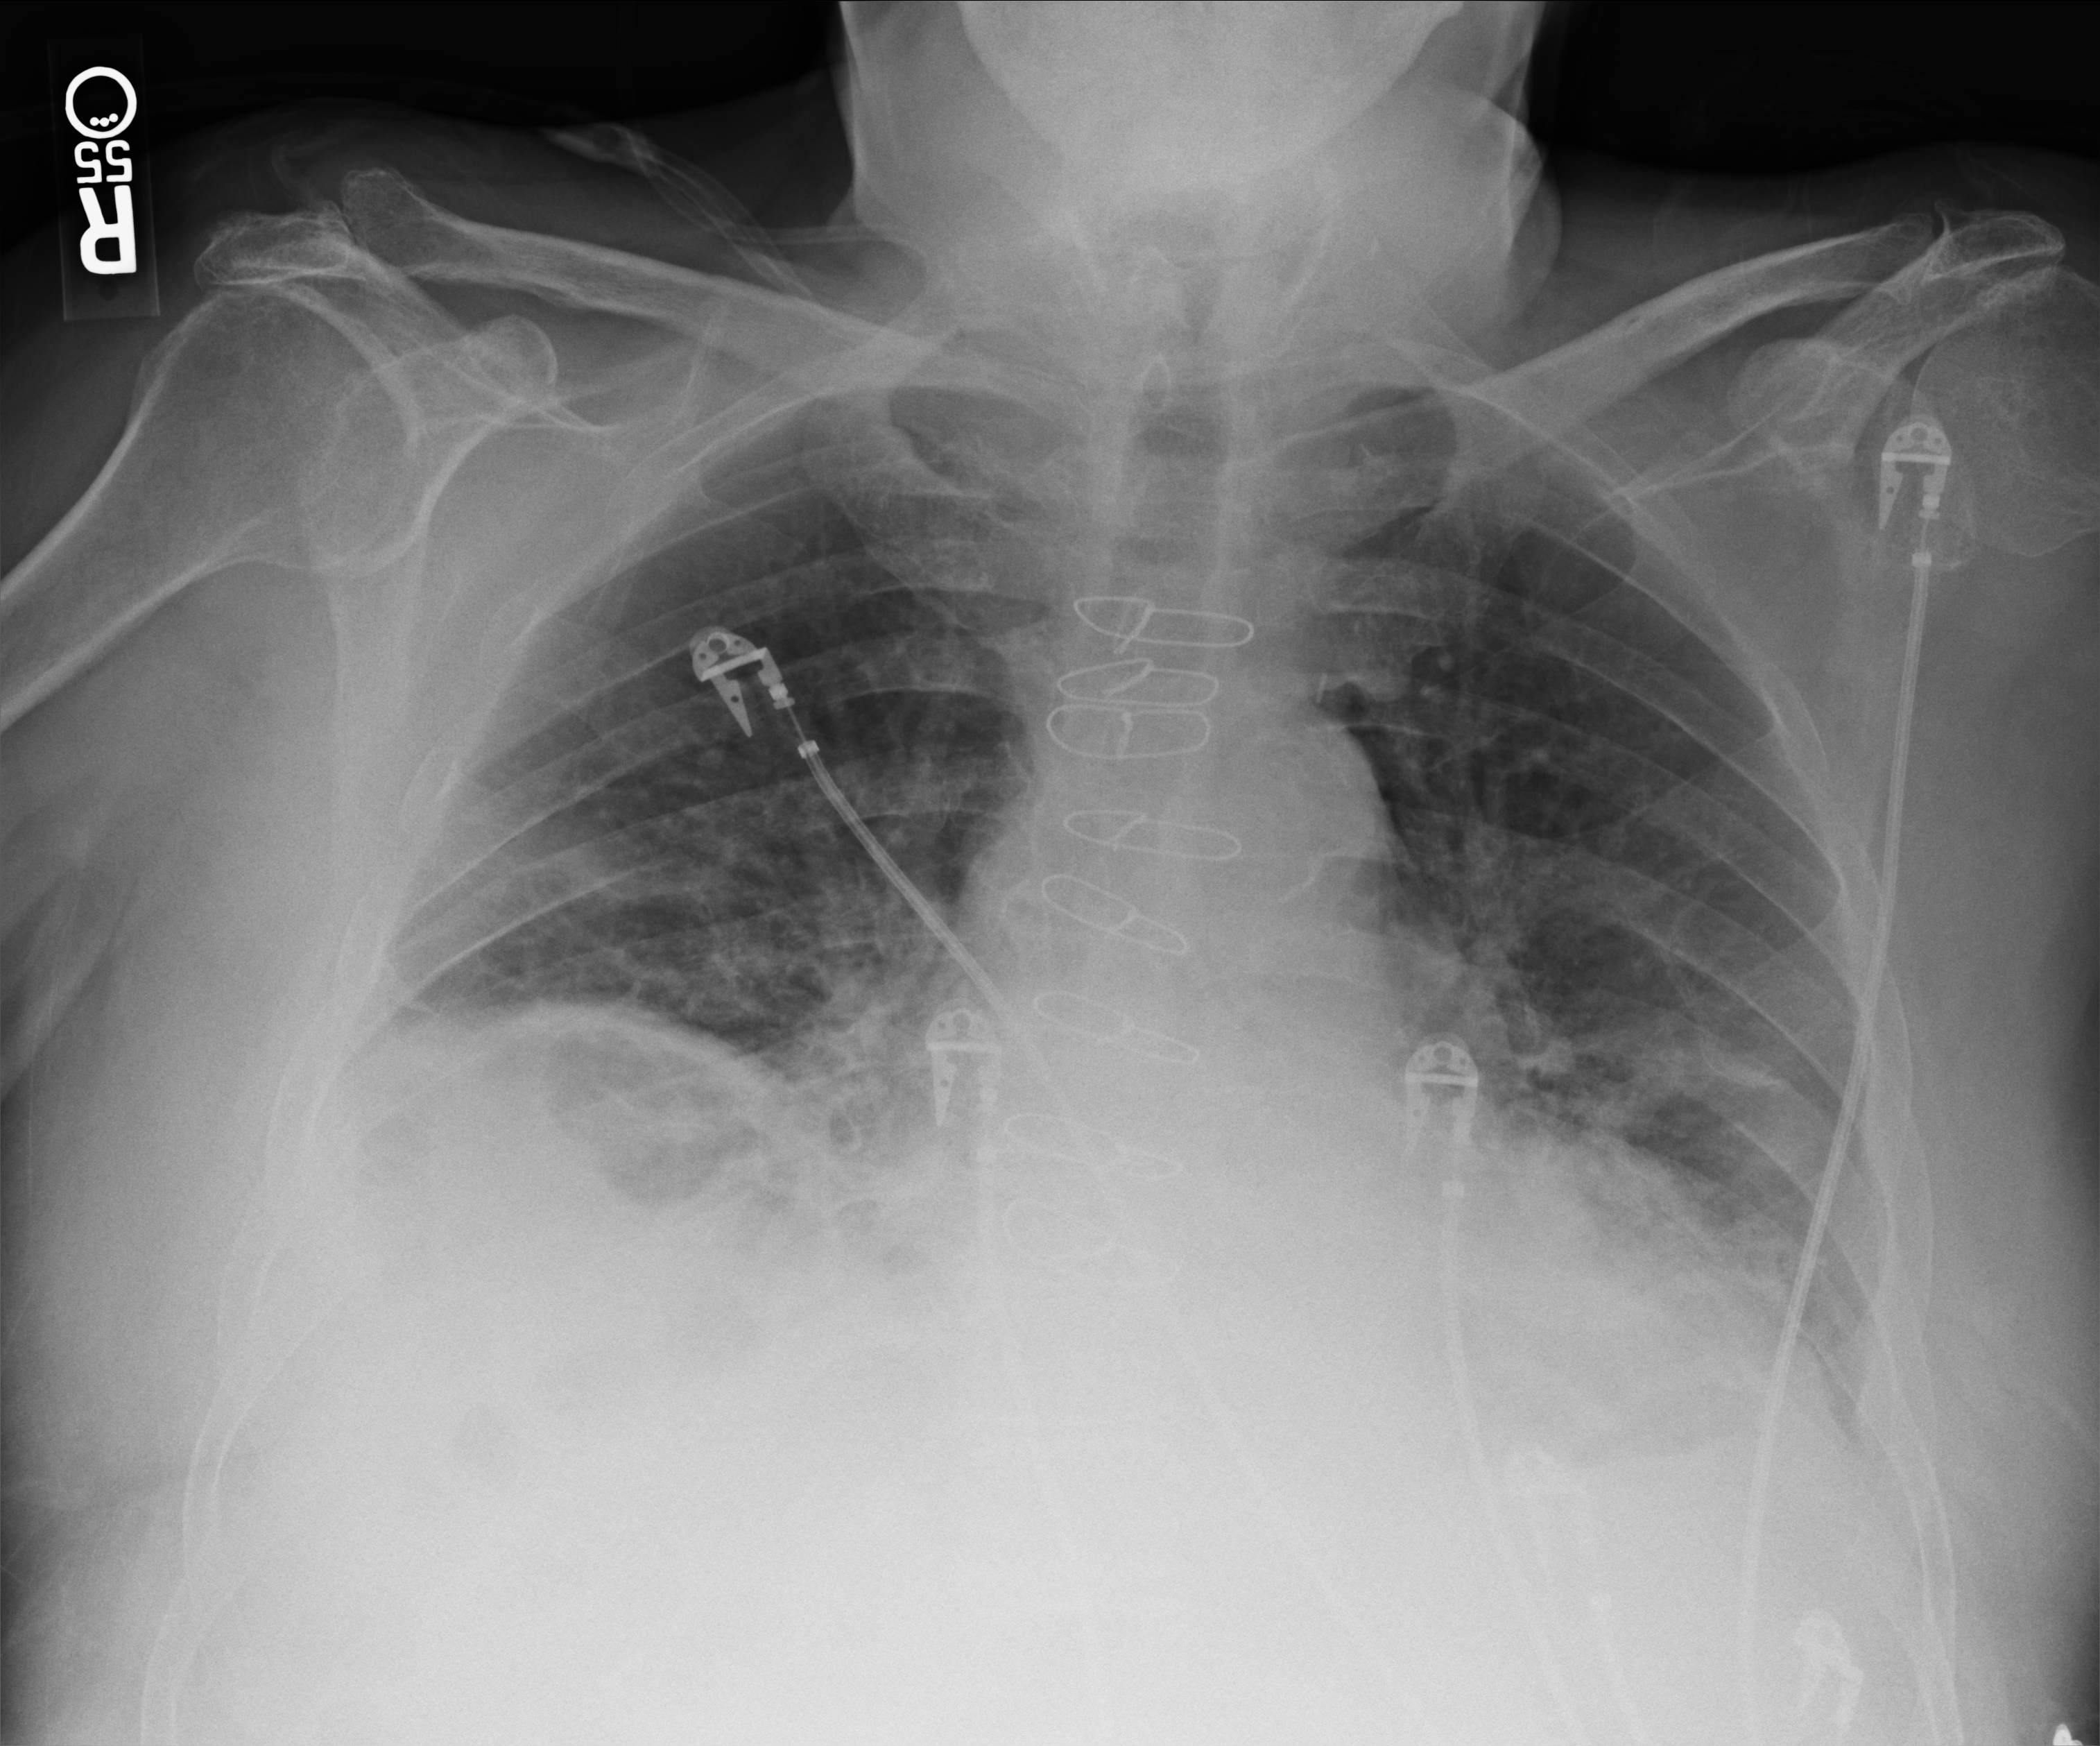
Chest X-ray (portable); anteroposterior (AP) projection. Male patient hospitalised with COVID-19, age 75–90 years.
Admission-level facts for this patient (not findings on this image; timing relative to this image not recorded): mechanically ventilated during this hospital stay: no; hypertension (admission record): yes.